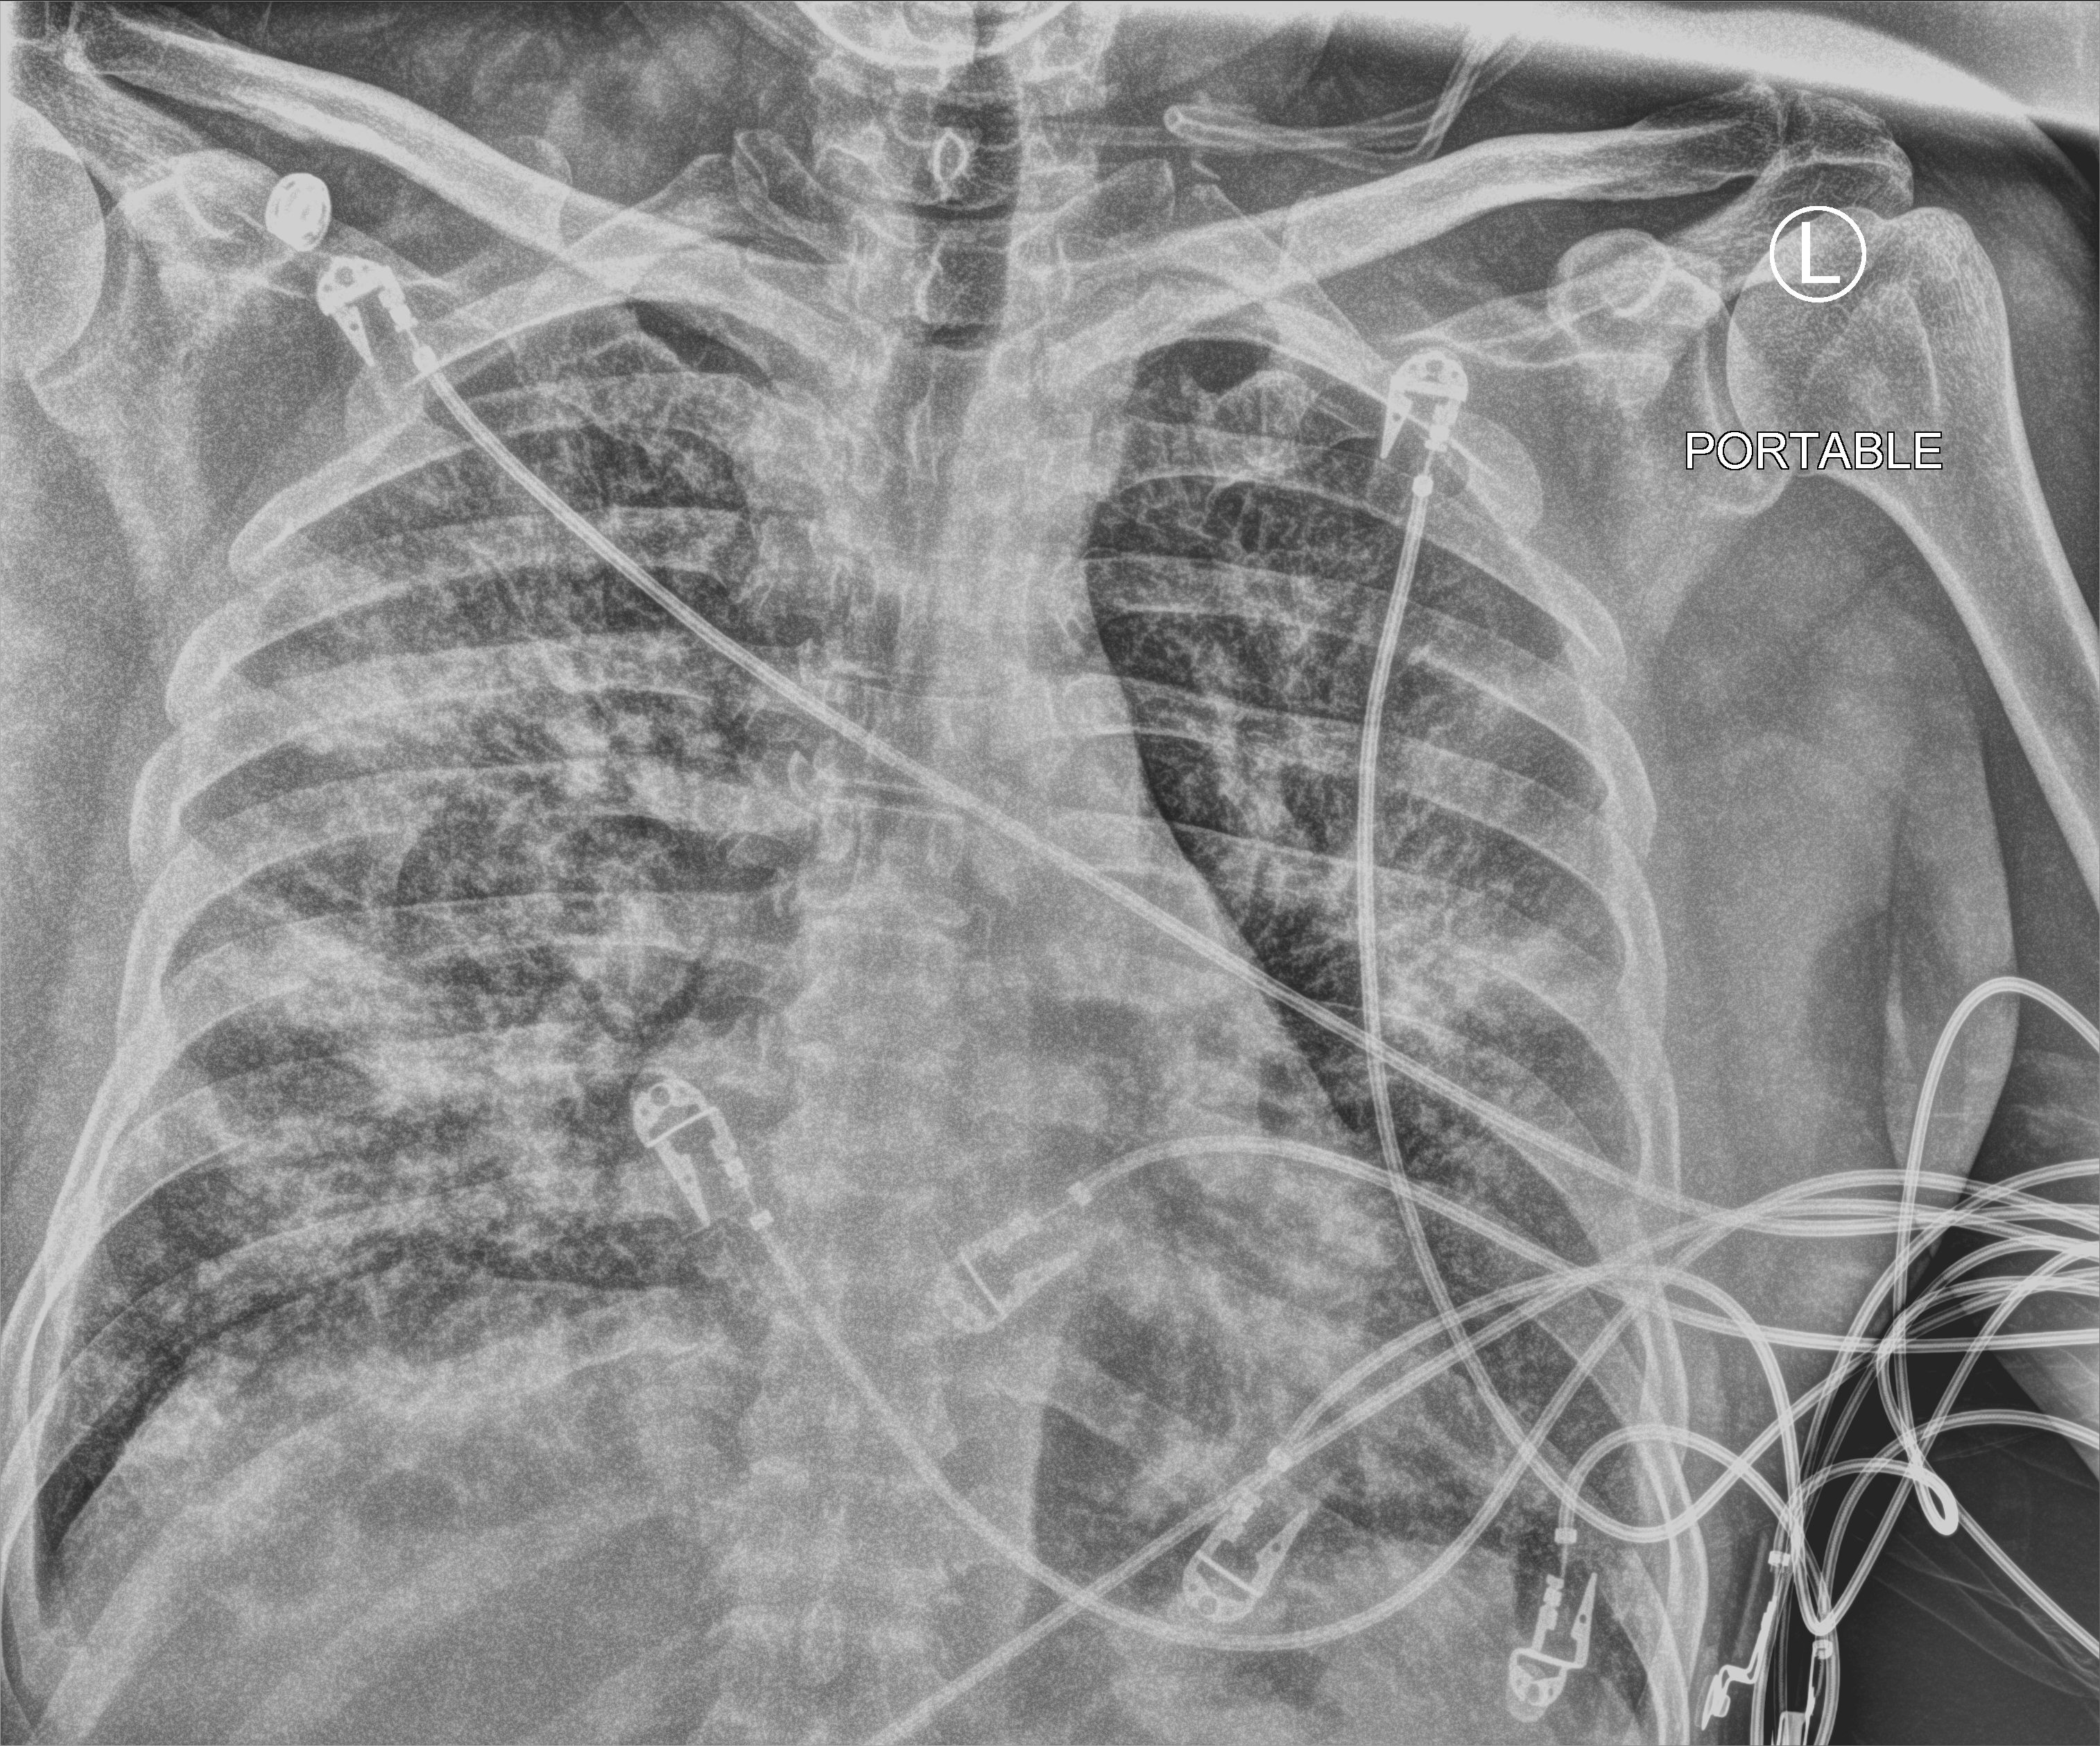
Portable chest radiograph, anteroposterior (AP) projection. Patient hospitalised with COVID-19; male, aged 18–59 years.
Admission-level facts for this patient (not findings on this image; timing relative to this image not recorded):
- diabetes (admission record): no
- mechanically ventilated during this hospital stay: no
- admitted to intensive care during this hospital stay: yes